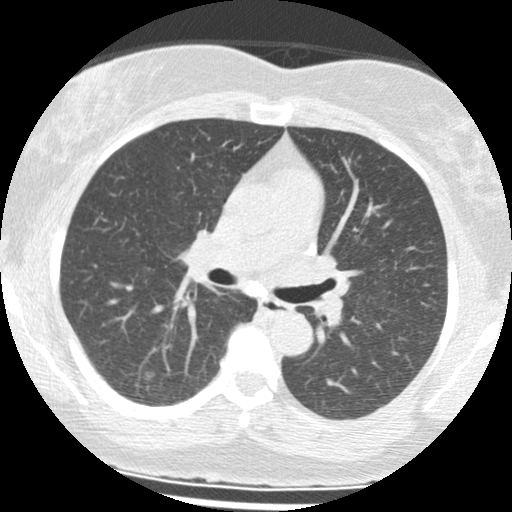
Axial slice from a low-dose chest CT screening exam; baseline screening round; lung window (W 1500 / L -600 HU); 2.5 mm slice thickness; slice 49 of 124 in the series; 512 × 512 image matrix. Female, age 65 years at enrolment. Current smoker at enrolment.
Expert reader's lesion annotation, bounding box [x1, y1, x2, y2] px = [127, 359, 165, 392]. The exam's reader record, not a measurement of the box and not confirmed to be the same lesion: non-calcified nodule or mass ≥4 mm, right lower lobe, 8 × 6 mm, poorly defined margins, mixed attenuation. Participant outcome: lung cancer diagnosed 423 days after this screen — non-small cell carcinoma, right lower lobe, well differentiated (G1), stage IA (AJCC 6th edition), 10 mm at pathology.